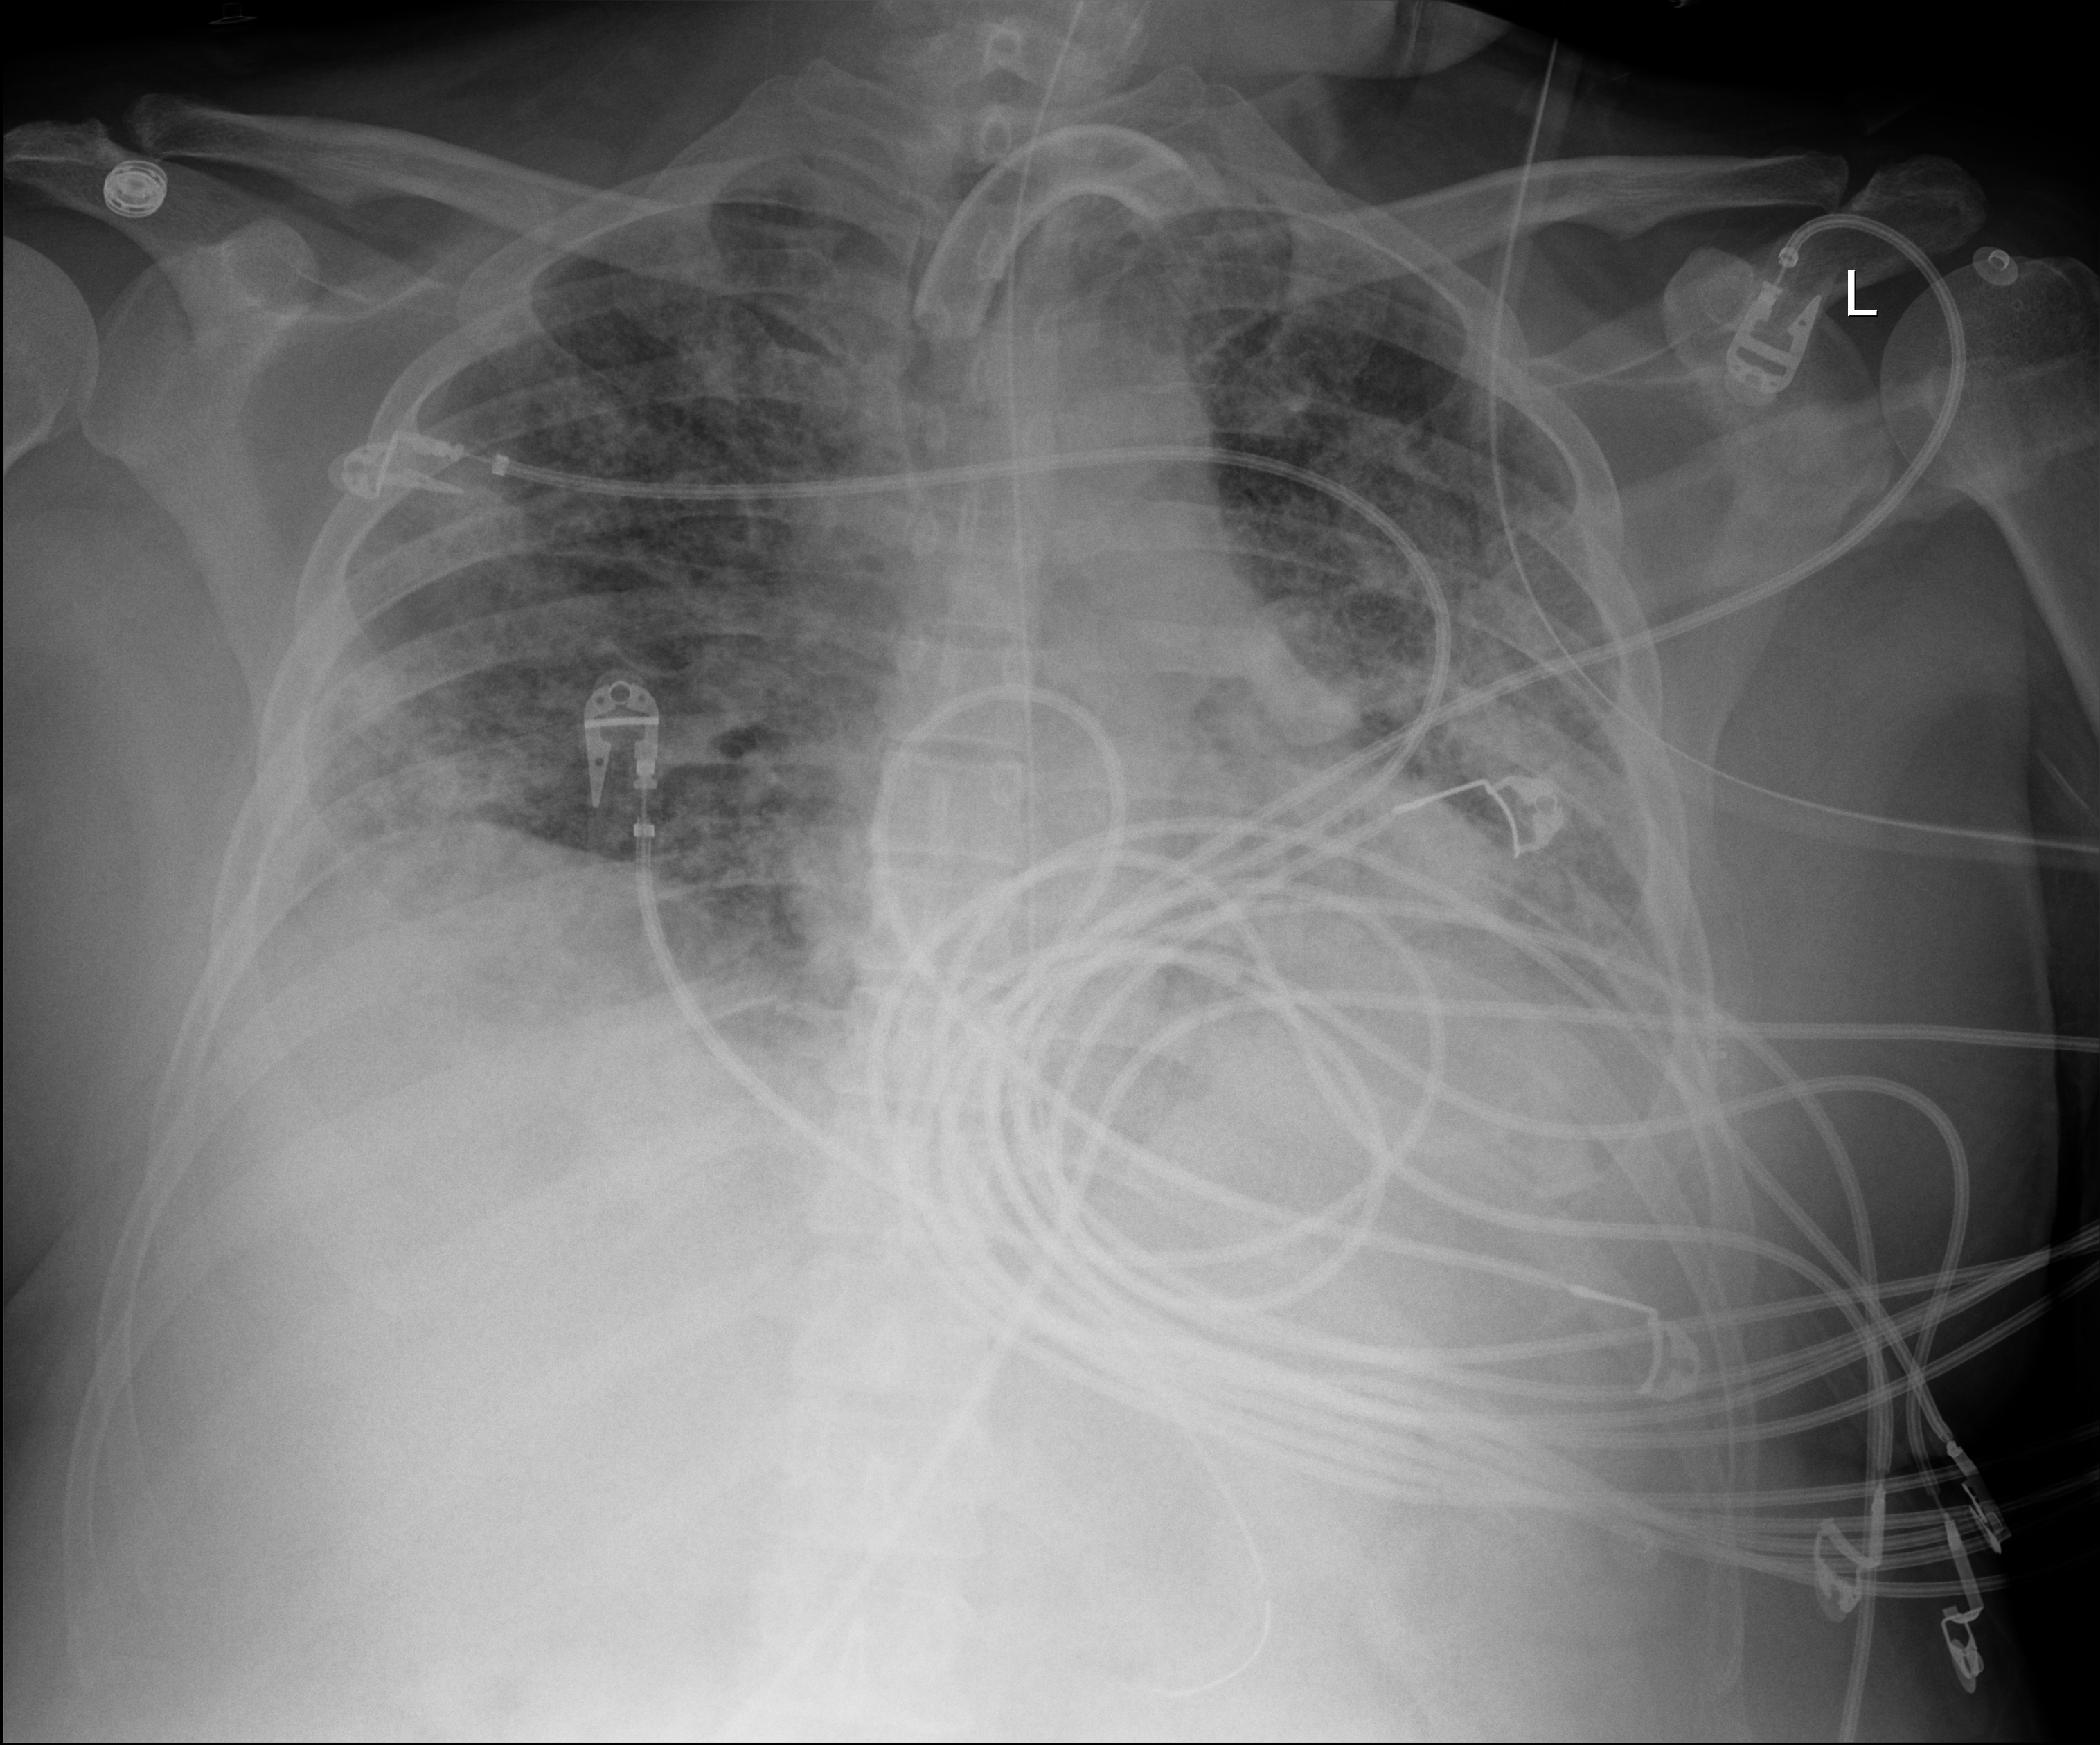
Portable chest radiograph; anteroposterior (AP) projection. Male patient hospitalised with COVID-19, age 18–59 years.
Hospital-stay facts (about this admission, not read from this image; timing relative to this image not recorded): diabetes (admission record): no; mechanically ventilated during this hospital stay: yes.